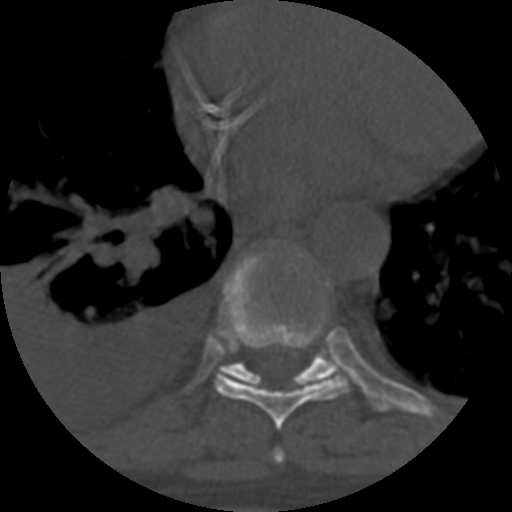
CT including the spine, one axial slice. Position 390 of 708 along the scan axis. 120 kVp. One of 3 acquisitions stored at this slice position. Bone window (W 1800 / L 400 HU). 512 × 512 image matrix. Patient age 55 years. Case-level facts recorded for this patient, not image findings: primary cancer: colon.
Structures marked on this image (semi-automatically segmented with operator editing):
- T7 vertebra: box from (x=272, y=449) to (x=285, y=464) px
- T8 vertebra: (x=214, y=256)–(x=351, y=430)
- T9 vertebra: (x=218, y=253)–(x=339, y=388)